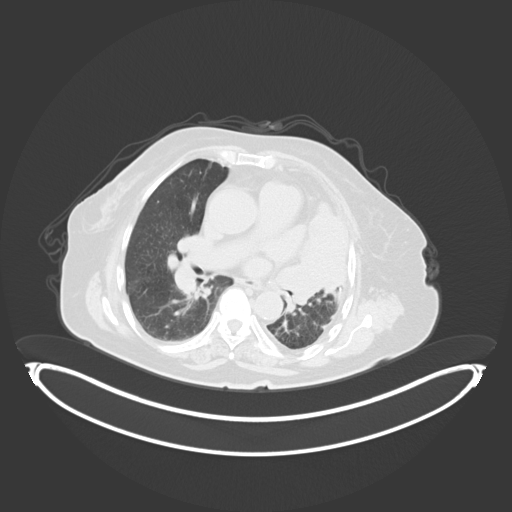
Chest CT, one axial slice. Position 197 of 284 along the scan axis. Reconstruction kernel B30f. 120 kVp. Lung window (W 1500 / L -600 HU). 3 mm slice thickness. 512 × 512 image matrix, field of view 500 × 500 mm. Patient: female, 75 years. Case-level facts recorded for this patient, not image findings: clinical TNM (as recorded): T3 N3 M1.
Outlined on this slice (rectangle marked by the reading radiologist):
- lung tumour (recorded histology: adenocarcinoma): bounding box (x1, y1, x2, y2) in pixels: (276, 197, 351, 304)